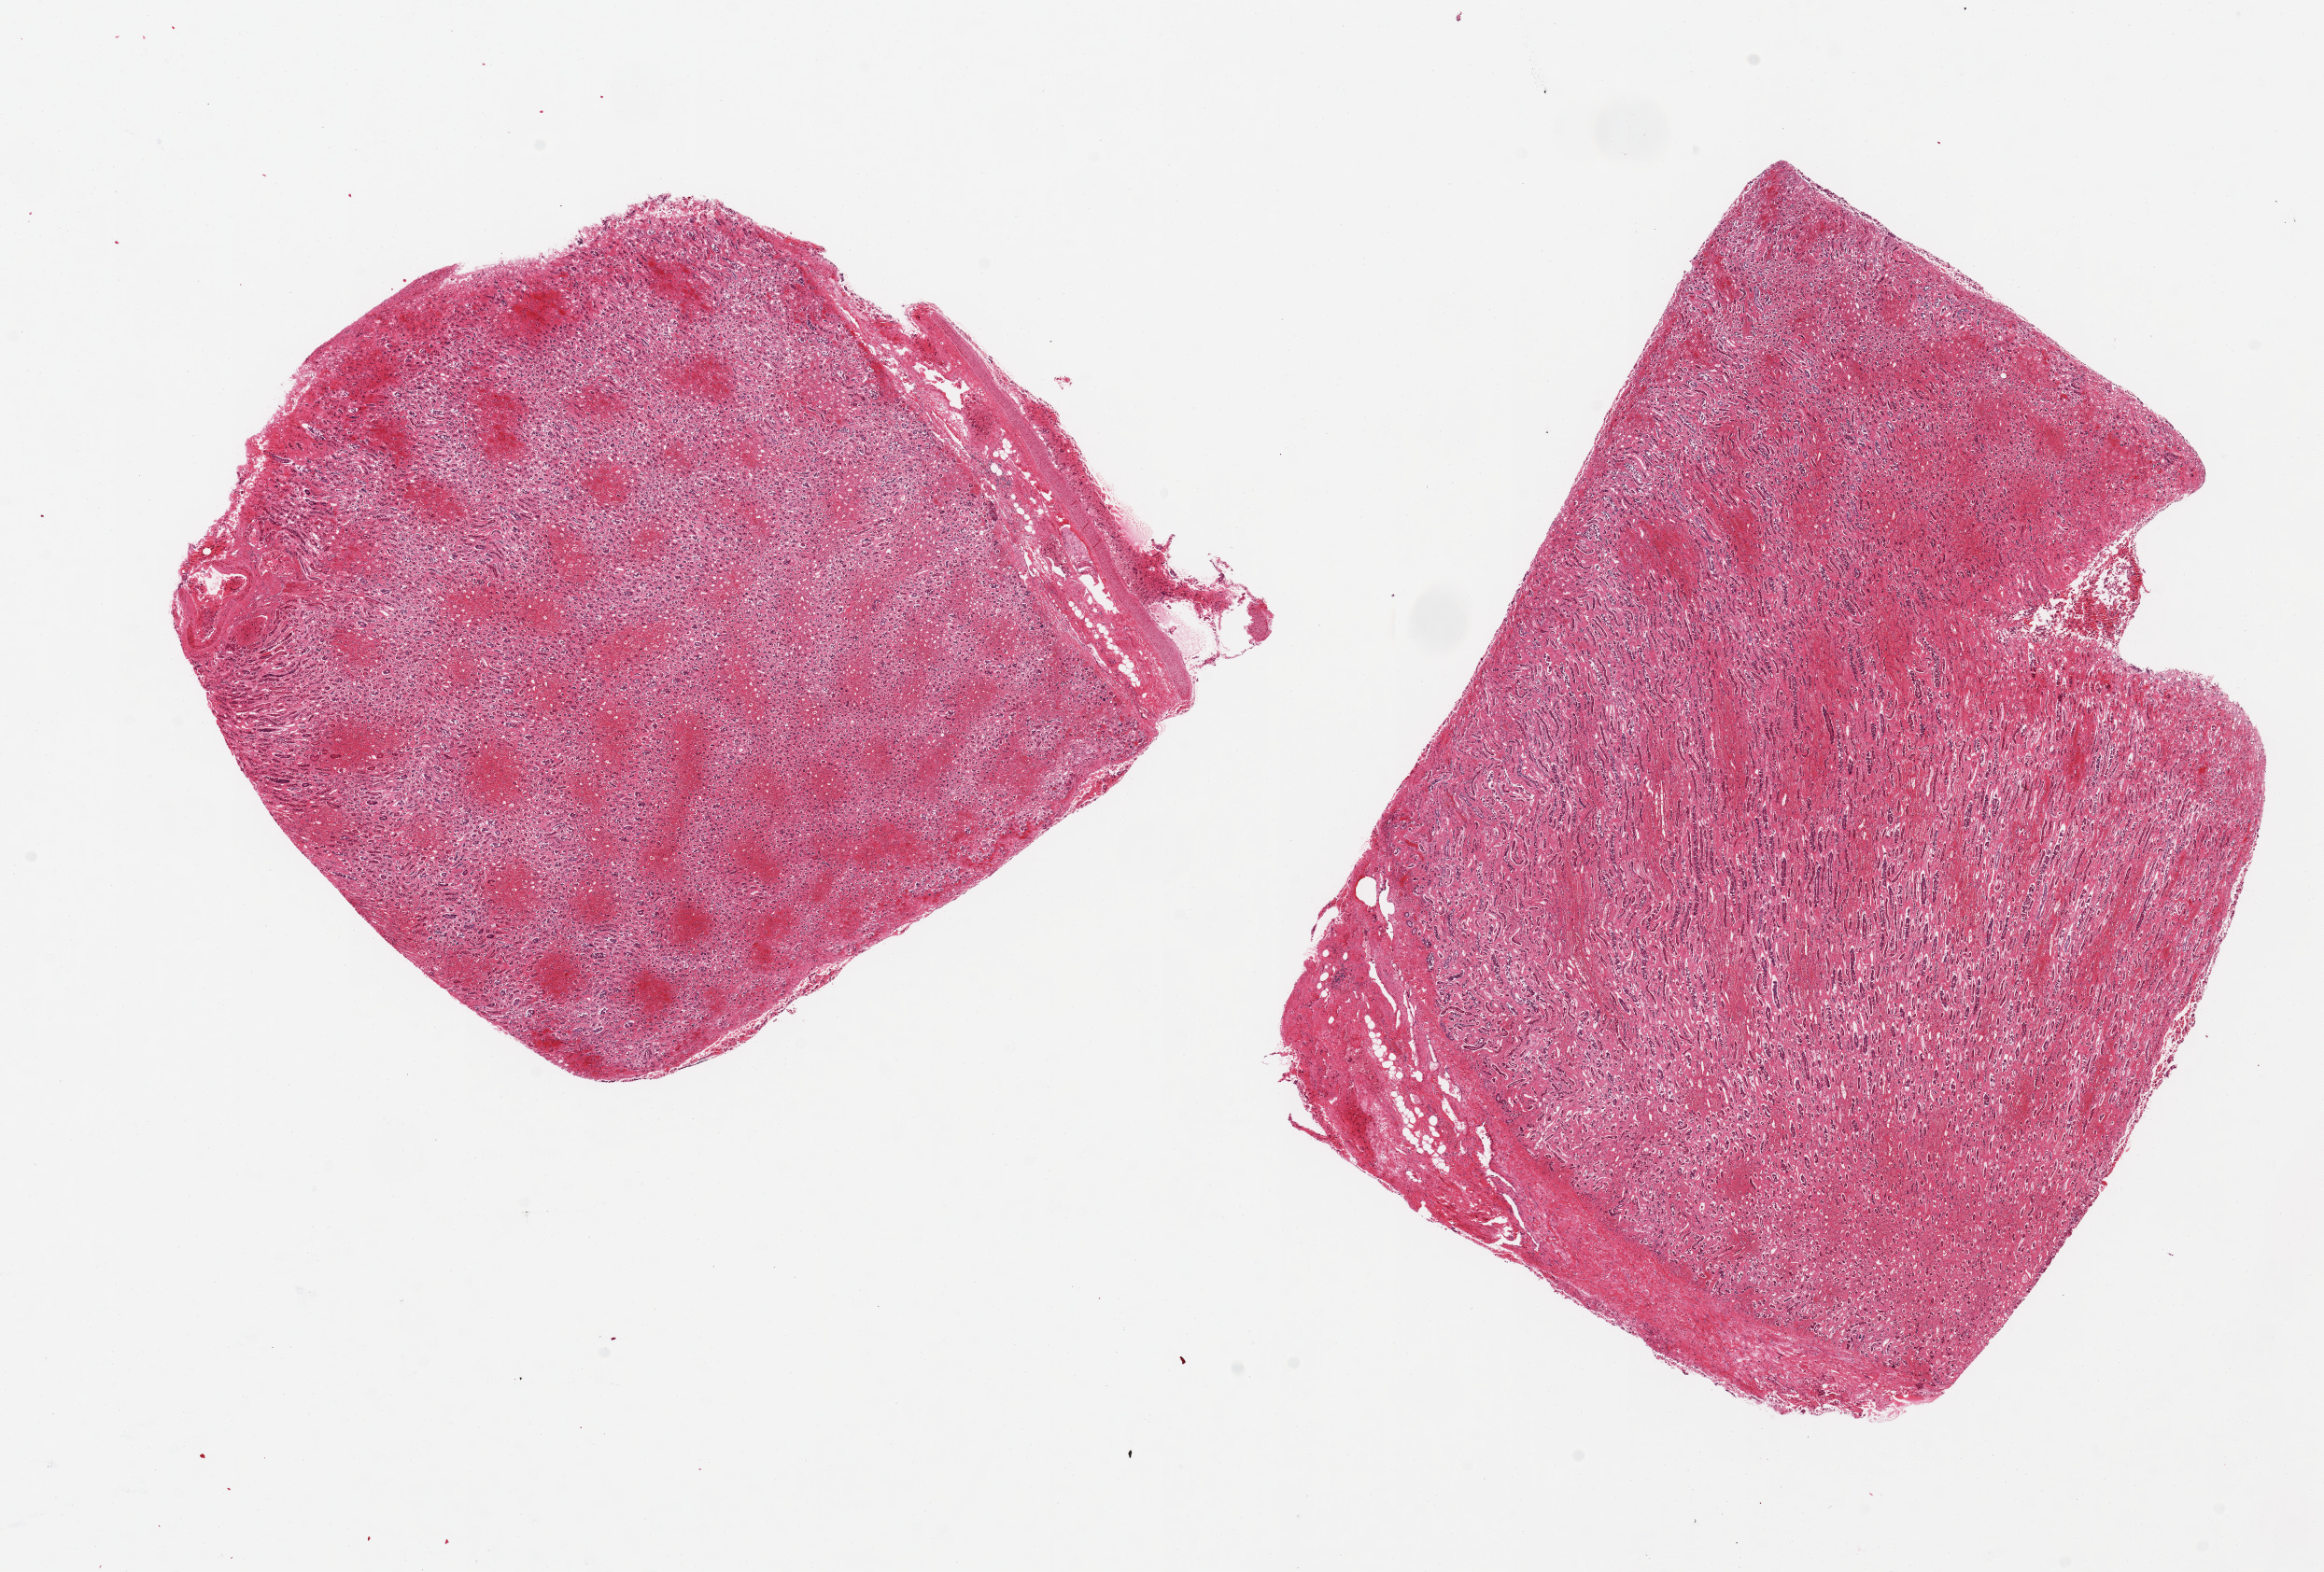
H&E whole-slide image, brightfield — low-resolution overview of the scanned area, about 19.7 x 13.3 mm, PAXgene-fixed paraffin-embedded (PFPE) section, target tissue: renal medulla, donor tissue sample. Male donor.
* reviewer comment on this tissue sample: 2 pieces 9x6 & 6x6 mm; all medulla, no cortex, many red cell casts